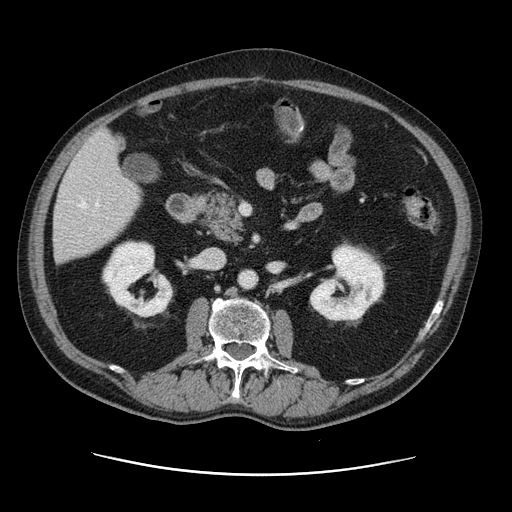
Contrast-enhanced abdominal CT, one axial slice. Position 50 of 141 along the scan axis. 120 kVp. Soft-tissue window (W 400 / L 40 HU). 2.5 mm slice thickness. 512 × 512 image matrix, field of view 395 × 395 mm. Male patient, age 72 years. From the clinical record (not read from this slice): diagnosis: colorectal cancer liver metastases, imaged before liver resection; multiple liver metastases: yes; largest metastasis: 5.4 cm.
Structures marked on this image (expert manual segmentation):
- hepatic veins: bounding box <78,200,99,229> (left, top, right, bottom; pixels)
- liver: <54,132,141,262>
- planned liver remnant (the part of the liver to remain after resection): <54,166,141,262>